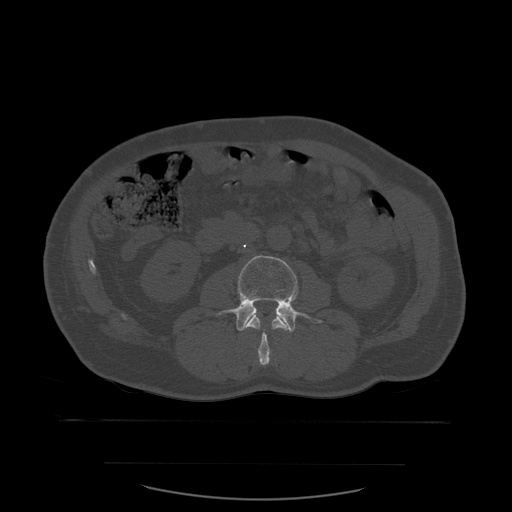
CT including the spine, one axial slice; slice 201 of 590 in the series (ordered by position); bone window (W 1800 / L 400 HU); 1.25 mm slice thickness; 512 × 512 image matrix, field of view 479 × 479 mm. Patient age 71 years. From the clinical record (not read from this slice): primary cancer: lung; vertebrae with lytic lesions (as recorded): T1, T2, L5, S1.
Outlined on this slice (semi-automatic segmentation, software-assisted and operator-edited):
- L2 vertebra: bounding box (x1, y1, x2, y2) in pixels: (245, 309, 291, 366)
- L3 vertebra: (217, 255, 323, 333)